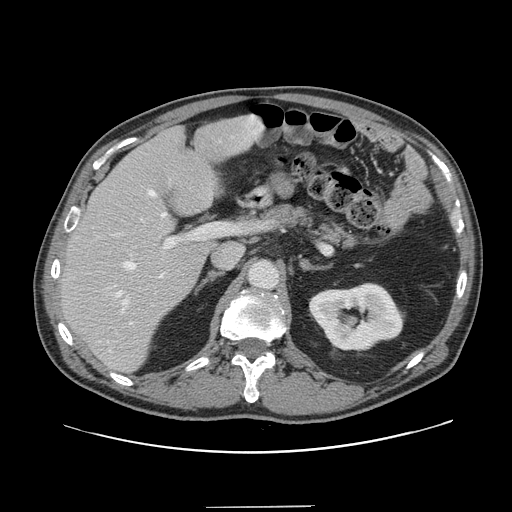
Contrast-enhanced abdominal CT, one axial slice; slice 88 of 139 in the series (ordered by position); 120 kVp; intravenous contrast given; soft-tissue window (W 400 / L 40 HU); 2.5 mm slice thickness; 512 × 512 image matrix, field of view 397 × 397 mm. Male patient, age 64 years. Case-level facts recorded for this patient, not image findings: diagnosis: colorectal cancer liver metastases, imaged before liver resection; multiple liver metastases: yes; largest metastasis: 3.5 cm.
Annotated regions visible in this slice (outlined manually by an expert reader):
- hepatic veins: bounding box <115,134,256,324> (left, top, right, bottom; pixels)
- liver: <61,116,262,371>
- planned liver remnant (the part of the liver to remain after resection): <62,116,262,371>
- portal vein (with intrahepatic branches): <114,222,218,313>